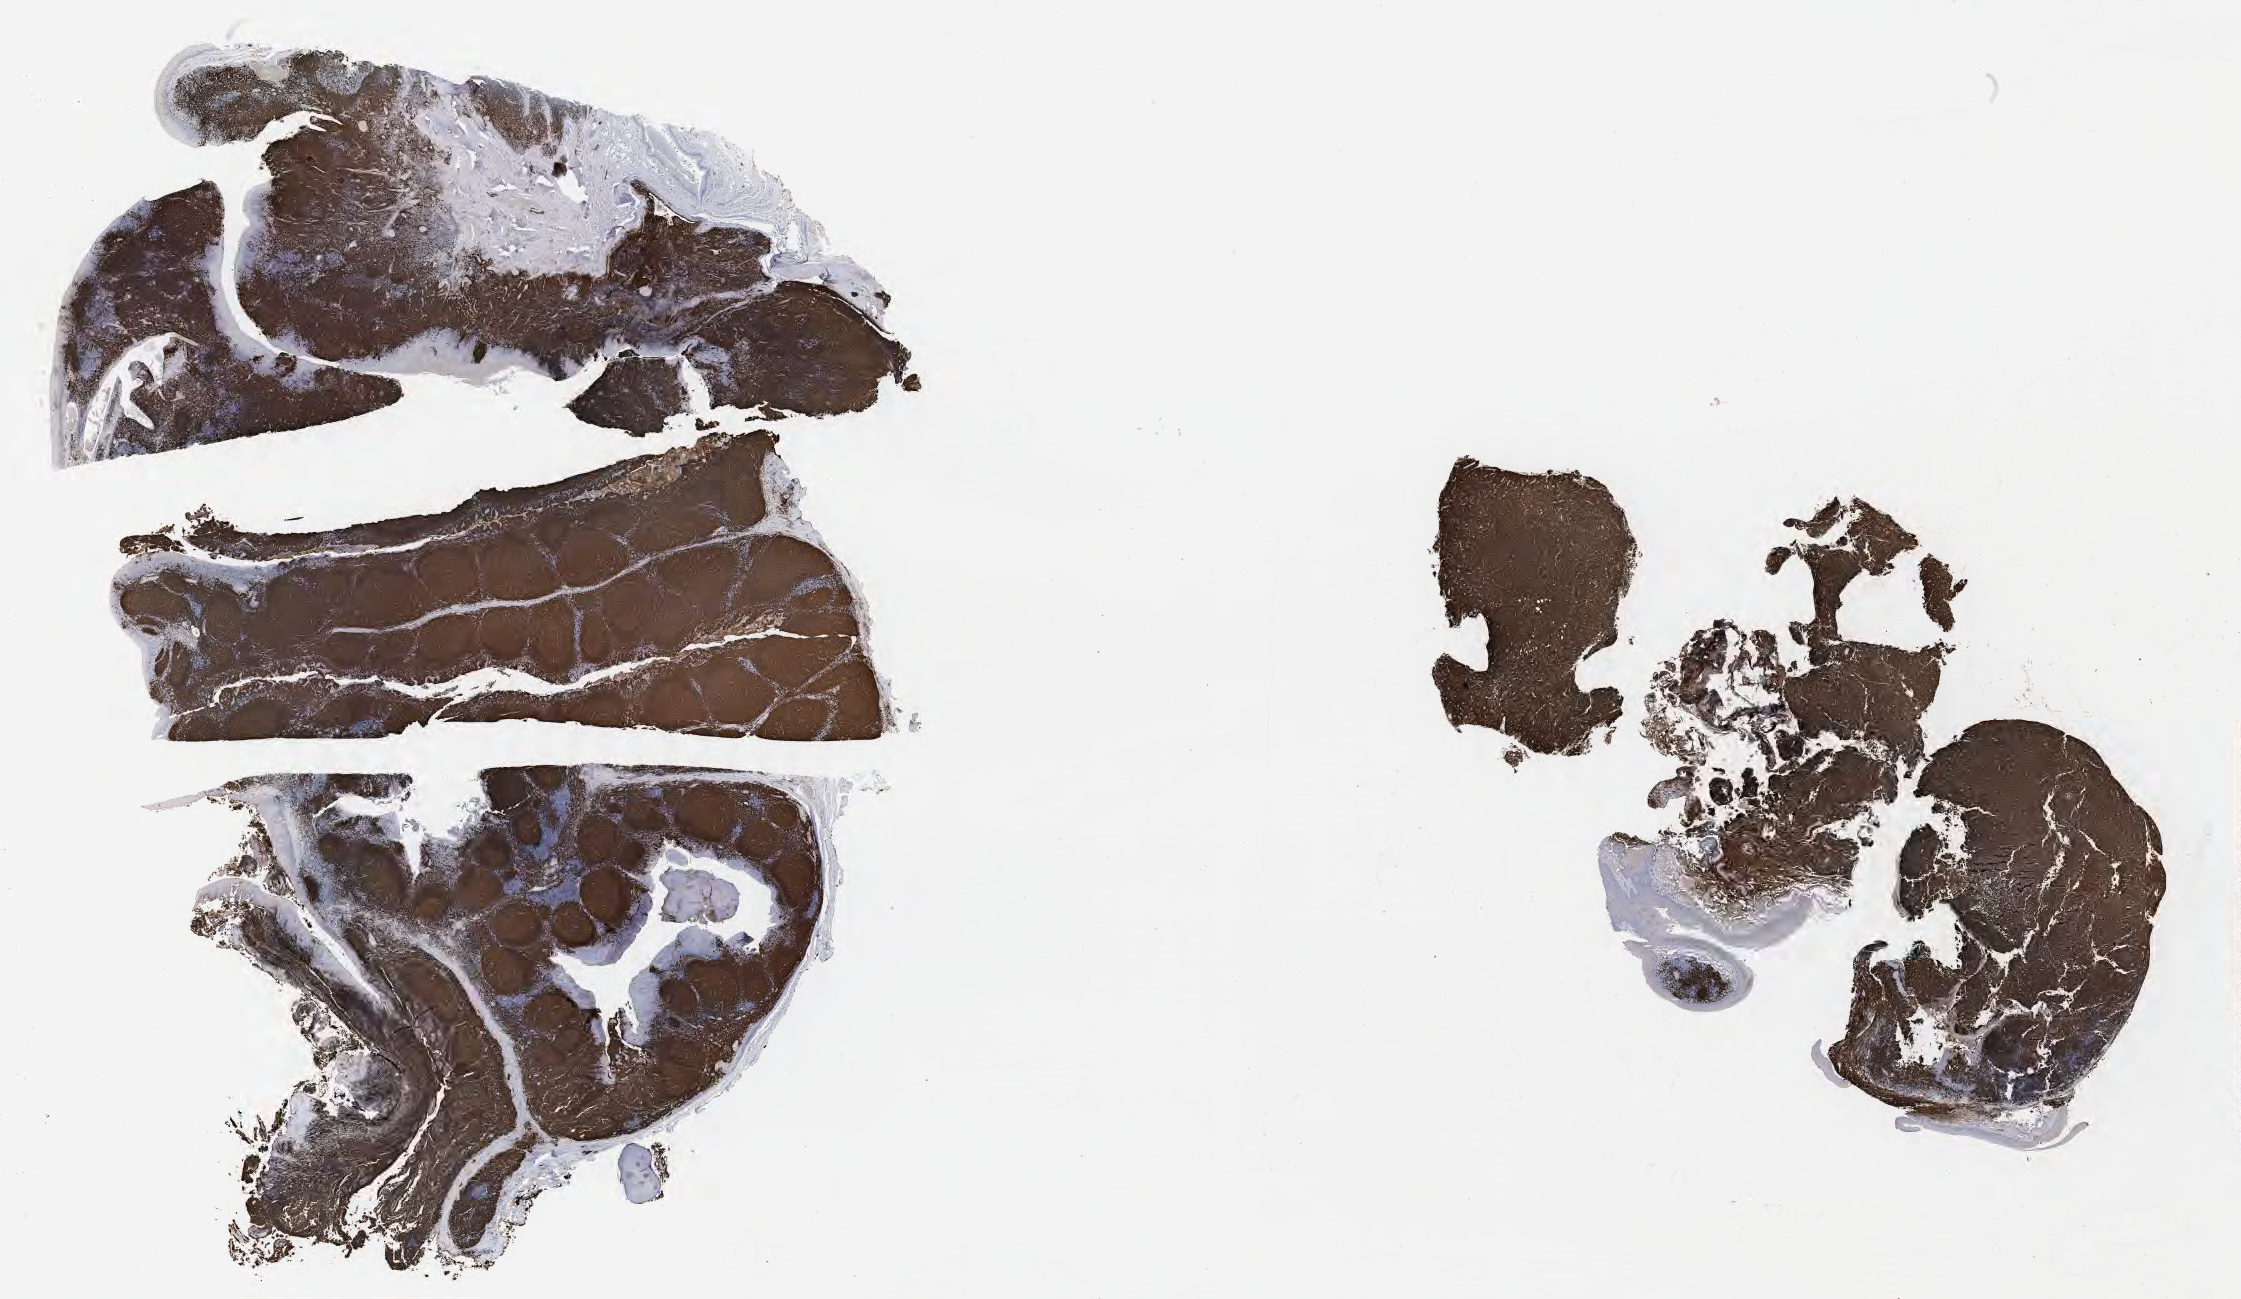
IHC for CD20, whole-slide image — a low-resolution overview of the entire scanned area, about 36.2 x 21.0 mm. Tumor tissue. Male patient, aged 63.
Diagnosis: Burkitt lymphoma, NOS.